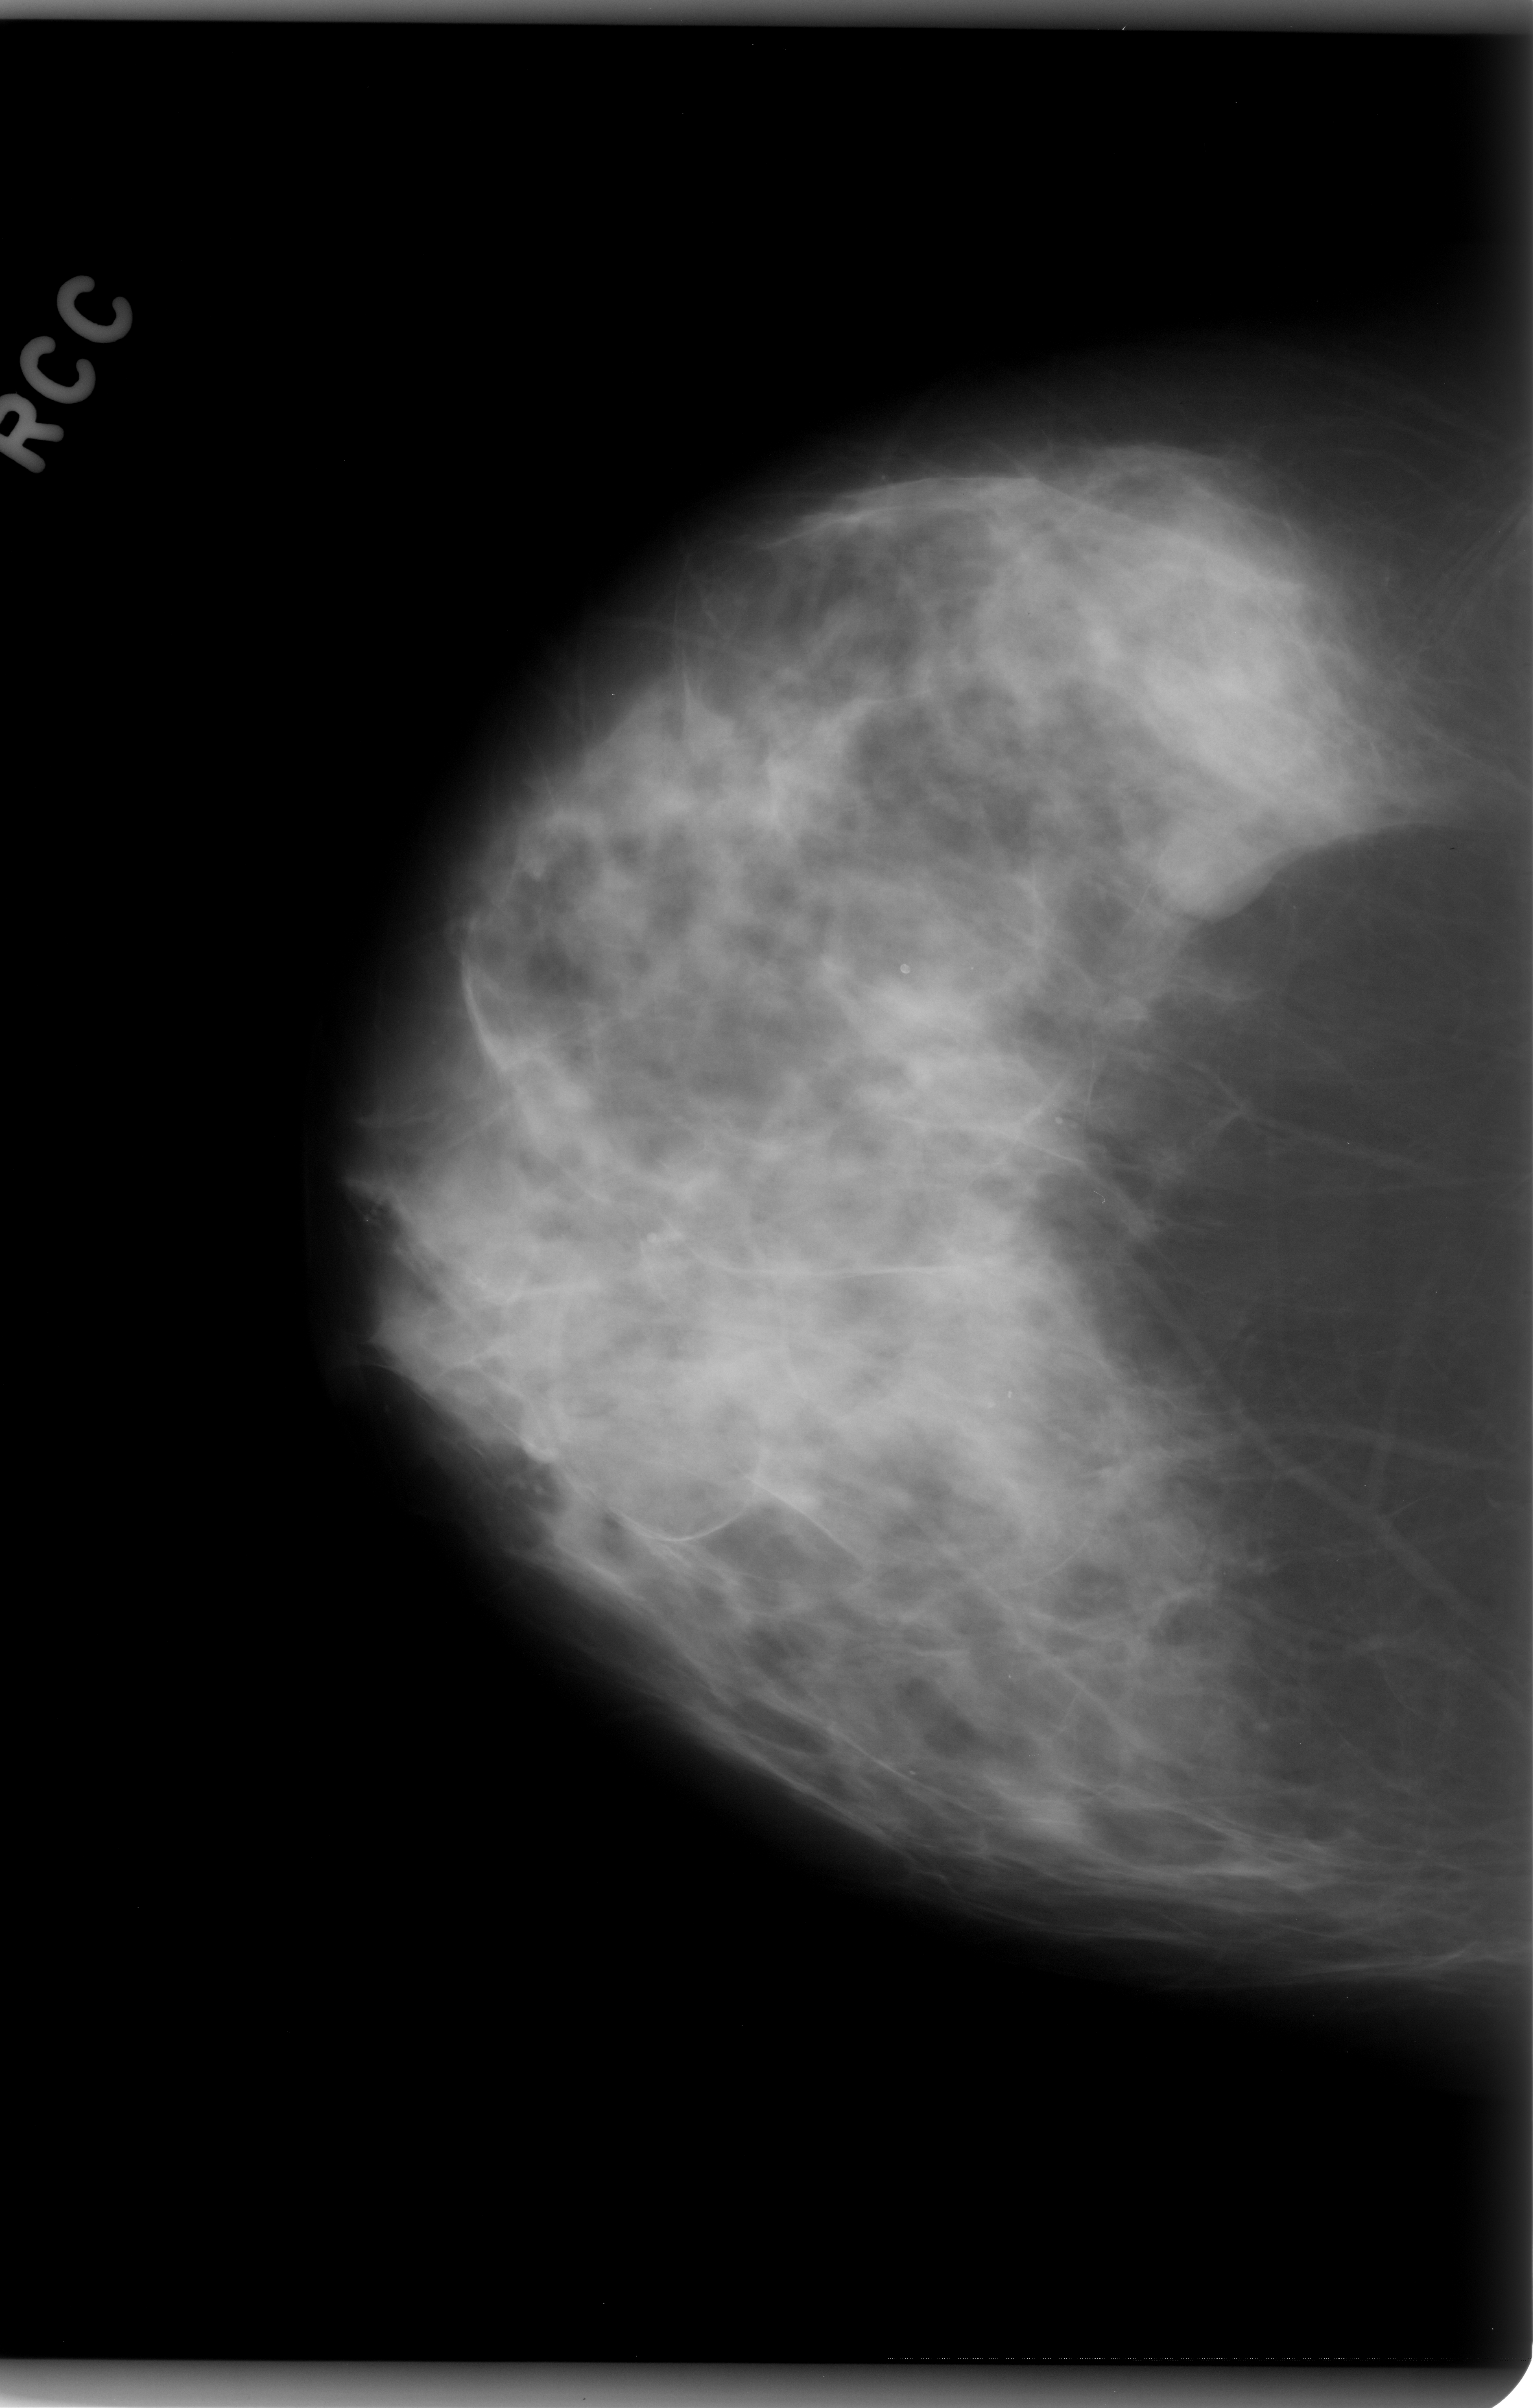
Digitized screen-film mammogram. Right breast. Craniocaudal (CC) view. BI-RADS breast density category 3 (scale 1–4). 1533 × 2408 image matrix.
Marked abnormalities (boxes around the expert regions of interest):
- mass, shape oval, margins circumscribed; BI-RADS assessment category 4; subtlety rating 5 on a 1 (subtle) to 5 (obvious) scale; pathology result (as recorded, not read from the image): benign: box from (x=1117, y=809) to (x=1291, y=931) px